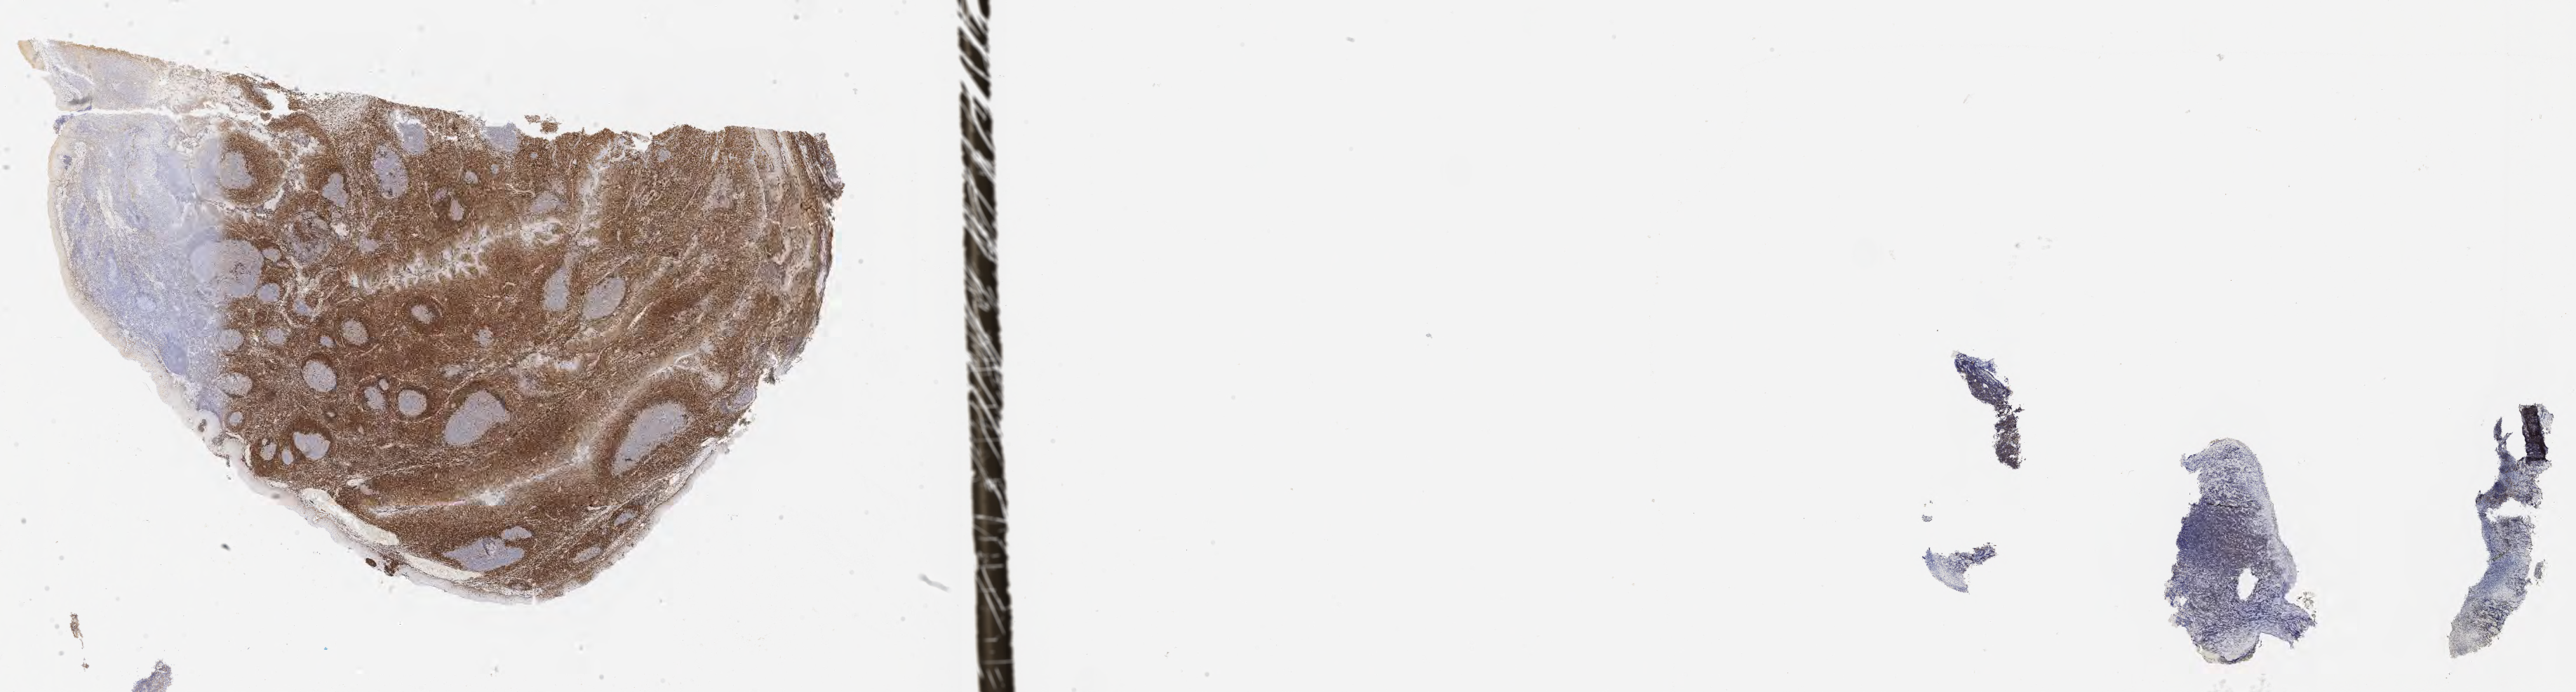
IHC for BCL2, whole-slide image — low-resolution overview of the scanned area, about 29.7 x 8.0 mm; specimen: tumor tissue; anatomic site: colon. Patient male; age 28 years.
- histologic diagnosis: Burkitt lymphoma, NOS